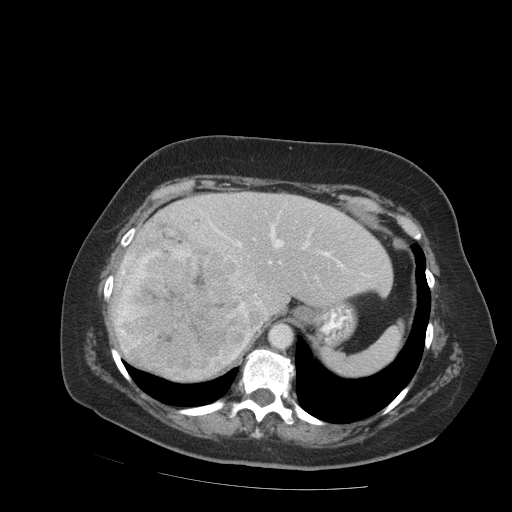
Contrast-enhanced abdominal CT (liver protocol), one axial slice; slice 66 of 99 in the series (ordered by position); reconstruction kernel STANDARD; 140 kVp; soft-tissue window (W 400 / L 40 HU); 2.5 mm slice thickness; 512 × 512 image matrix, field of view 400 × 400 mm. Case-level facts recorded for this patient, not image findings: diagnosis: hepatocellular carcinoma (patient treated with transarterial chemoembolisation; whether this scan precedes or follows treatment is not stated here); TNM stage (as recorded): Stage-IVB; Child-Pugh class: A; tumour differentiation: moderately differentiated.
Structures marked on this image (semi-automatically segmented with operator editing):
- abdominal aorta: bounding box (x1, y1, x2, y2) in pixels: (269, 323, 293, 348)
- liver parenchyma outside the tumour (the mass and vessels are separate outlines, so this box may not span the whole liver): (114, 192, 392, 340)
- mass: (111, 224, 263, 382)
- liver vessels: (127, 211, 370, 305)